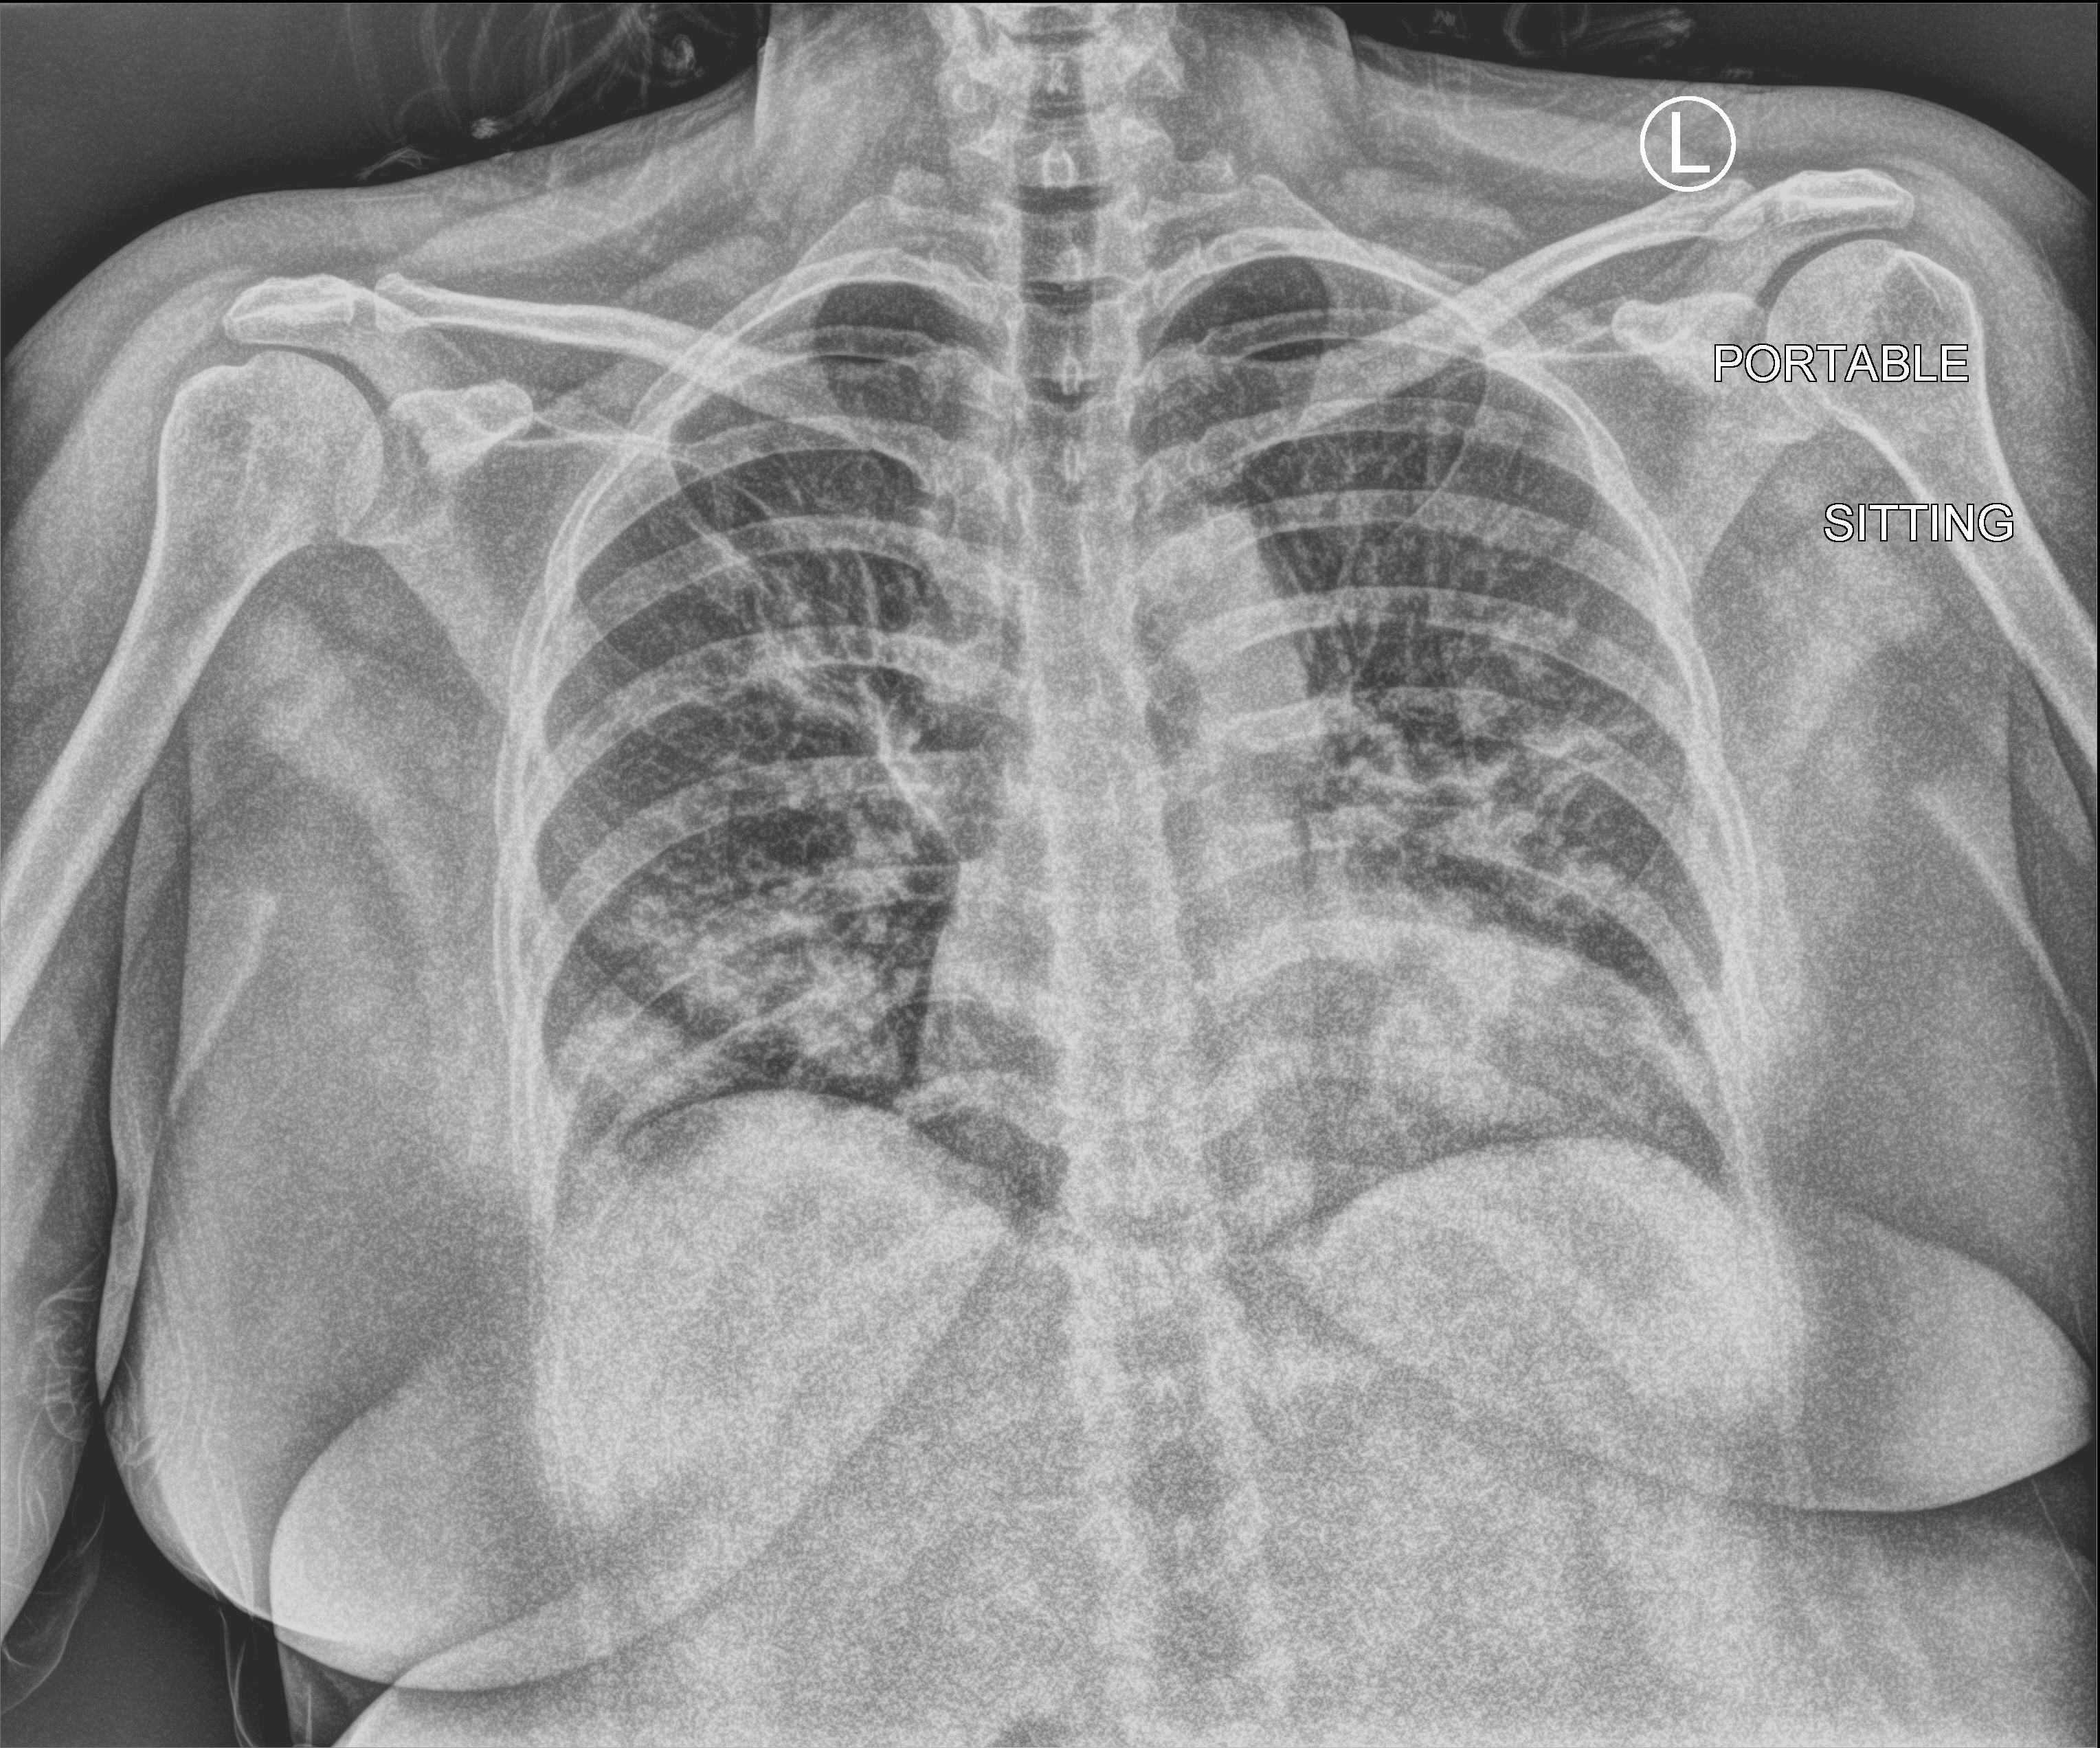
Chest X-ray (portable); anteroposterior (AP) projection. Patient hospitalised with COVID-19; female, aged 18–59 years.
From the hospital-stay record, not from the radiograph (when in the stay this image was taken is not recorded): admitted to intensive care during this hospital stay: no; COPD (admission record): no.